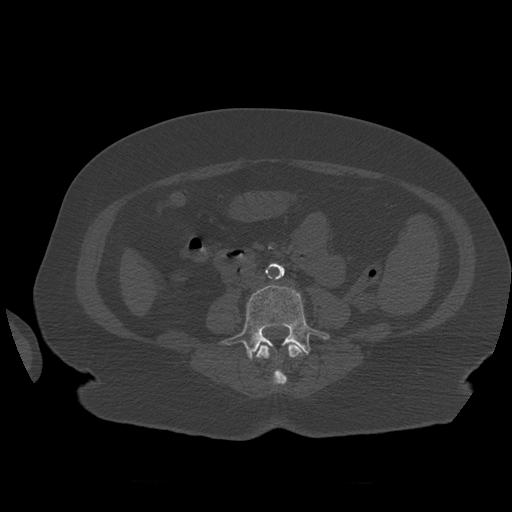
CT including the spine, one axial slice. 120 kVp. Bone window (W 1800 / L 400 HU). 1.25 mm slice thickness. 512 × 512 image matrix, field of view 404 × 404 mm. Patient age 81 years. Case-level facts recorded for this patient, not image findings: primary cancer: renal; vertebrae with lytic lesions (as recorded): L1.
Outlined on this slice (semi-automatically segmented with operator editing):
- L3 vertebra: box from (x=256, y=343) to (x=307, y=385) px
- L4 vertebra: (x=221, y=285)–(x=330, y=360)